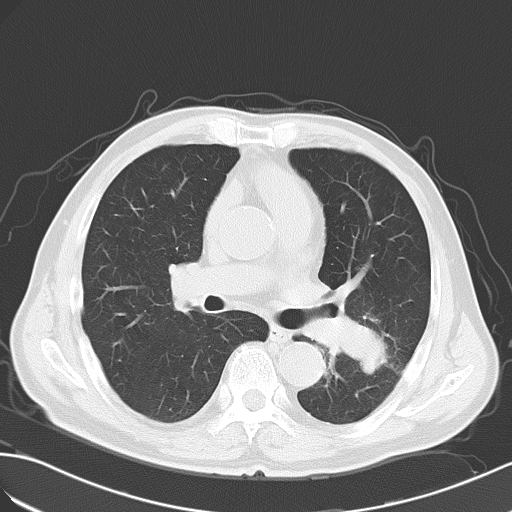
Chest CT, one axial slice; position 31 of 55 along the scan axis; 120 kVp; lung window (W 1500 / L -600 HU); 512 × 512 image matrix, field of view 353 × 353 mm. Patient: male, 63 years. From the clinical record (not read from this slice): clinical TNM (as recorded): T3 N3 M1a; histopathological grade: G3.
Structures marked on this image (rectangle marked by the reading radiologist):
- lung tumour (recorded histology: large cell carcinoma): box from (x=326, y=309) to (x=387, y=375) px